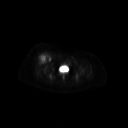
FDG PET of an extremity soft-tissue mass (from a PET/CT study), one axial slice; position 64 of 267 along the scan axis; 3.27 mm slice thickness; 128 × 128 image matrix, field of view 700 × 700 mm. Patient: female, 56 years. Case-level facts recorded for this patient, not image findings: histological type: malignant solitary fibrous tumor; grade: intermediate; site of the primary tumour: right thigh.
Structures marked on this image (expert contour drawn on MRI and transferred to this co-registered scan by the dataset authors):
- gross tumour volume including surrounding oedema: bounding box (x1, y1, x2, y2) in pixels: (36, 53, 49, 62)
- gross tumour volume (mass): (41, 54, 45, 58)